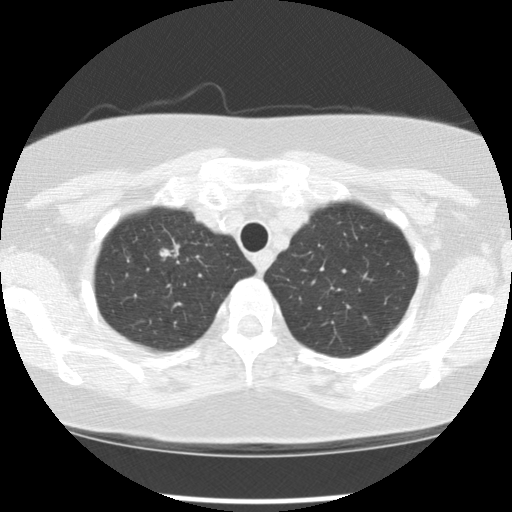
Low-dose screening chest CT, one axial slice; slice 97 of 113 in the series (ordered by position); reconstruction kernel STANDARD; lung window (W 1500 / L -600 HU); 2.5 mm slice thickness; 512 × 512 image matrix.
Outlined on this slice (outlined manually by an expert reader):
- lesion 1 (tumor, upper lobe of right lung): bounding box <159,248,172,260> (left, top, right, bottom; pixels)